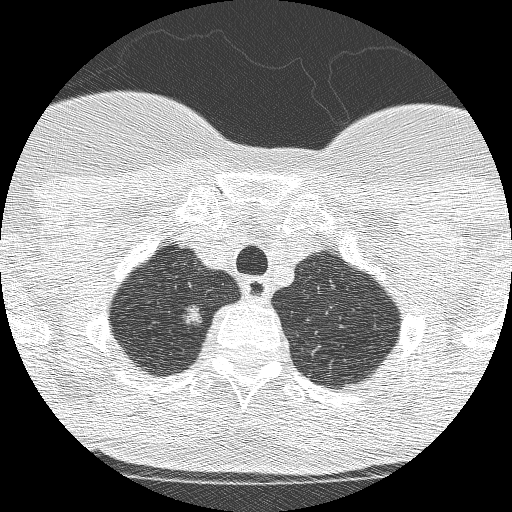
Chest CT (low-dose screening protocol), one axial image, second annual screen, lung window (W 1500 / L -600 HU), lung (sharp) reconstruction kernel (BONE), 512 × 512 image matrix, field of view 257 × 257 mm. Female participant, aged 61 years at enrolment.
Lesion marked by an expert reader, box from (x=165, y=298) to (x=214, y=337) px. The exam's reader record, not a measurement of the box and not confirmed to be the same lesion: non-calcified nodule or mass ≥4 mm, right upper lobe, 11 × 8 mm, poorly defined margins, mixed attenuation, pre-existing on the prior screen: yes; interval growth: yes. Official screen result: positive, change unspecified: nodule(s) >= 4 mm or enlarging nodule(s), mass(es), or other non-specific abnormalities suspicious for lung cancer. Lung cancer was diagnosed 28 days after this screen: adenocarcinoma, NOS, right upper lobe, poorly differentiated (G3), 12 mm at pathology.